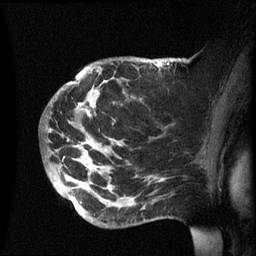
Breast MRI (dynamic contrast-enhanced), one sagittal slice. Position 40 of 60 along the scan axis. Dynamic contrast-enhanced series, image 2 of 3 at this slice position (ordered by acquisition). 1.5 T. TE 4.2 ms, TR 8.4 ms. 256 × 256 image matrix. Female patient, age 49 years.
Outlined on this slice (semi-automatically segmented with operator editing):
- analysis volume of interest (the breast-tissue region the enhancement analysis was run in; not a lesion): box from (x=44, y=57) to (x=174, y=228) px
- tumour enhancement mask (voxels above the 70 % enhancement threshold inside the analysis volume of interest): (x=81, y=62)–(x=169, y=158)